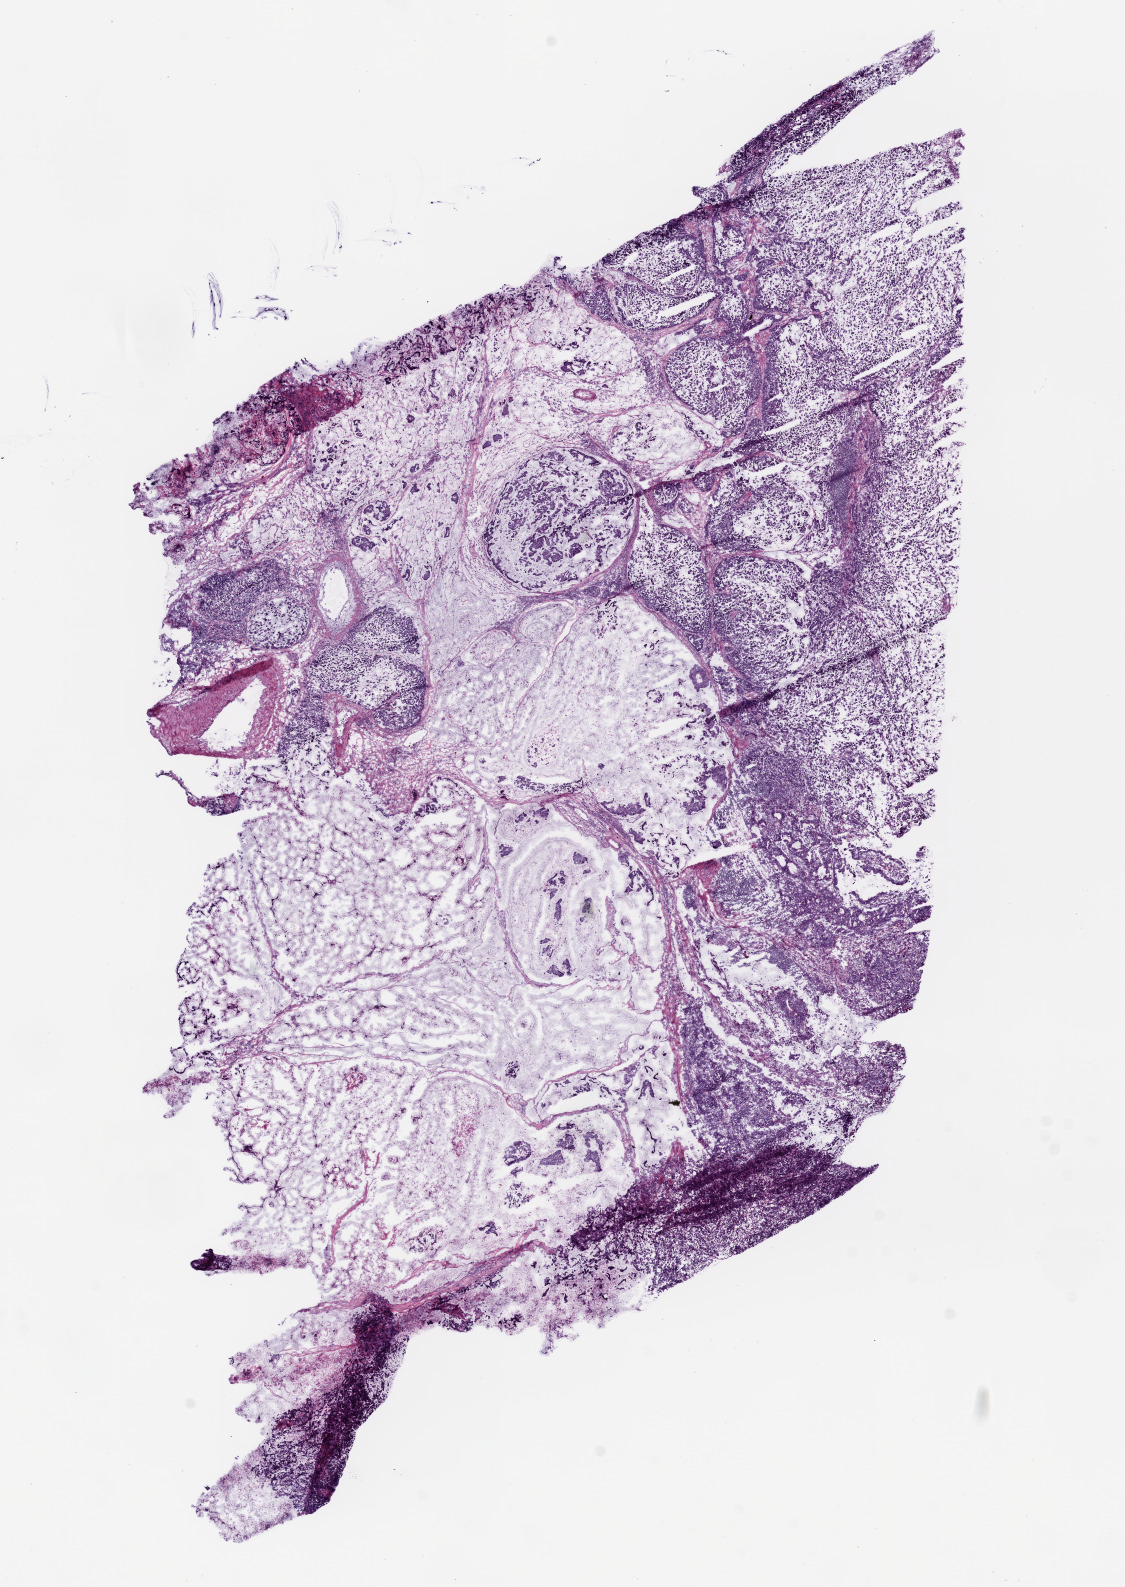
Digitized H&E-stained tissue section (whole slide) — low-resolution overview of the scanned area, about 9.0 x 12.7 mm (acquisition: 20x scan); frozen section from the top of the tissue portion; primary tumour sample from the stomach. Patient: male, age at initial diagnosis 76 years. Histologic grade: G3 (poorly differentiated). Pathologist review of this section (percent, as recorded): tumour cells 95%, tumour nuclei 75%, normal cells 0%, stromal cells 5%, necrosis 0%.
AJCC pathologic stage: IIIA (6th edition). Pathologic diagnosis: Adenocarcinoma, intestinal type (body of stomach).